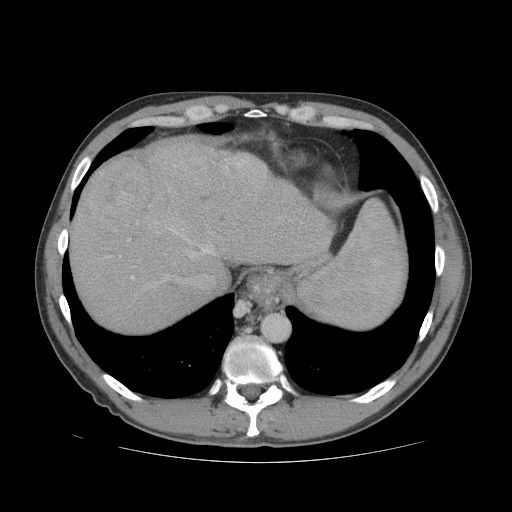
Contrast-enhanced abdominal CT (liver protocol), one axial slice. Position 62 of 81 along the scan axis. Soft-tissue window (W 400 / L 40 HU). 2.5 mm slice thickness. 512 × 512 image matrix, field of view 400 × 400 mm. Case-level facts recorded for this patient, not image findings: diagnosis: hepatocellular carcinoma (patient treated with transarterial chemoembolisation; whether this scan precedes or follows treatment is not stated here); TNM stage (as recorded): Stage-IVB; Child-Pugh class: B; tumour differentiation: well differentiated.
Outlined on this slice (semi-automatic segmentation, software-assisted and operator-edited):
- abdominal aorta: bounding box (x1, y1, x2, y2) in pixels: (262, 314, 289, 340)
- liver parenchyma outside the tumour (the mass and vessels are separate outlines, so this box may not span the whole liver): (68, 138, 333, 332)
- mass: (83, 157, 152, 232)
- liver vessels: (108, 159, 249, 279)